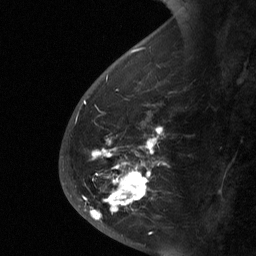
Breast MRI (dynamic contrast-enhanced), one sagittal slice; slice 19 of 64 in the series (ordered by position); dynamic contrast-enhanced study with each time point stored as its own series, time point 2 of 3 at this slice position (early post-contrast, ordered by acquisition time); 1.5 T; TE 4.8 ms, TR 27 ms; 2 mm slice thickness; 256 × 256 image matrix, field of view 180 × 180 mm. Female patient, age 56 years. From the clinical record (not read from this slice): setting: breast cancer imaged before/during neoadjuvant chemotherapy; receptor status: HER2-positive.
Structures marked on this image (semi-automatic segmentation, software-assisted and operator-edited):
- analysis volume of interest (the breast-tissue region the enhancement analysis was run in; not a lesion): bounding box [x1, y1, x2, y2] px = [59, 123, 172, 229]
- tumour enhancement mask (voxels above the 90 % enhancement threshold inside the analysis volume of interest): [85, 127, 163, 220]